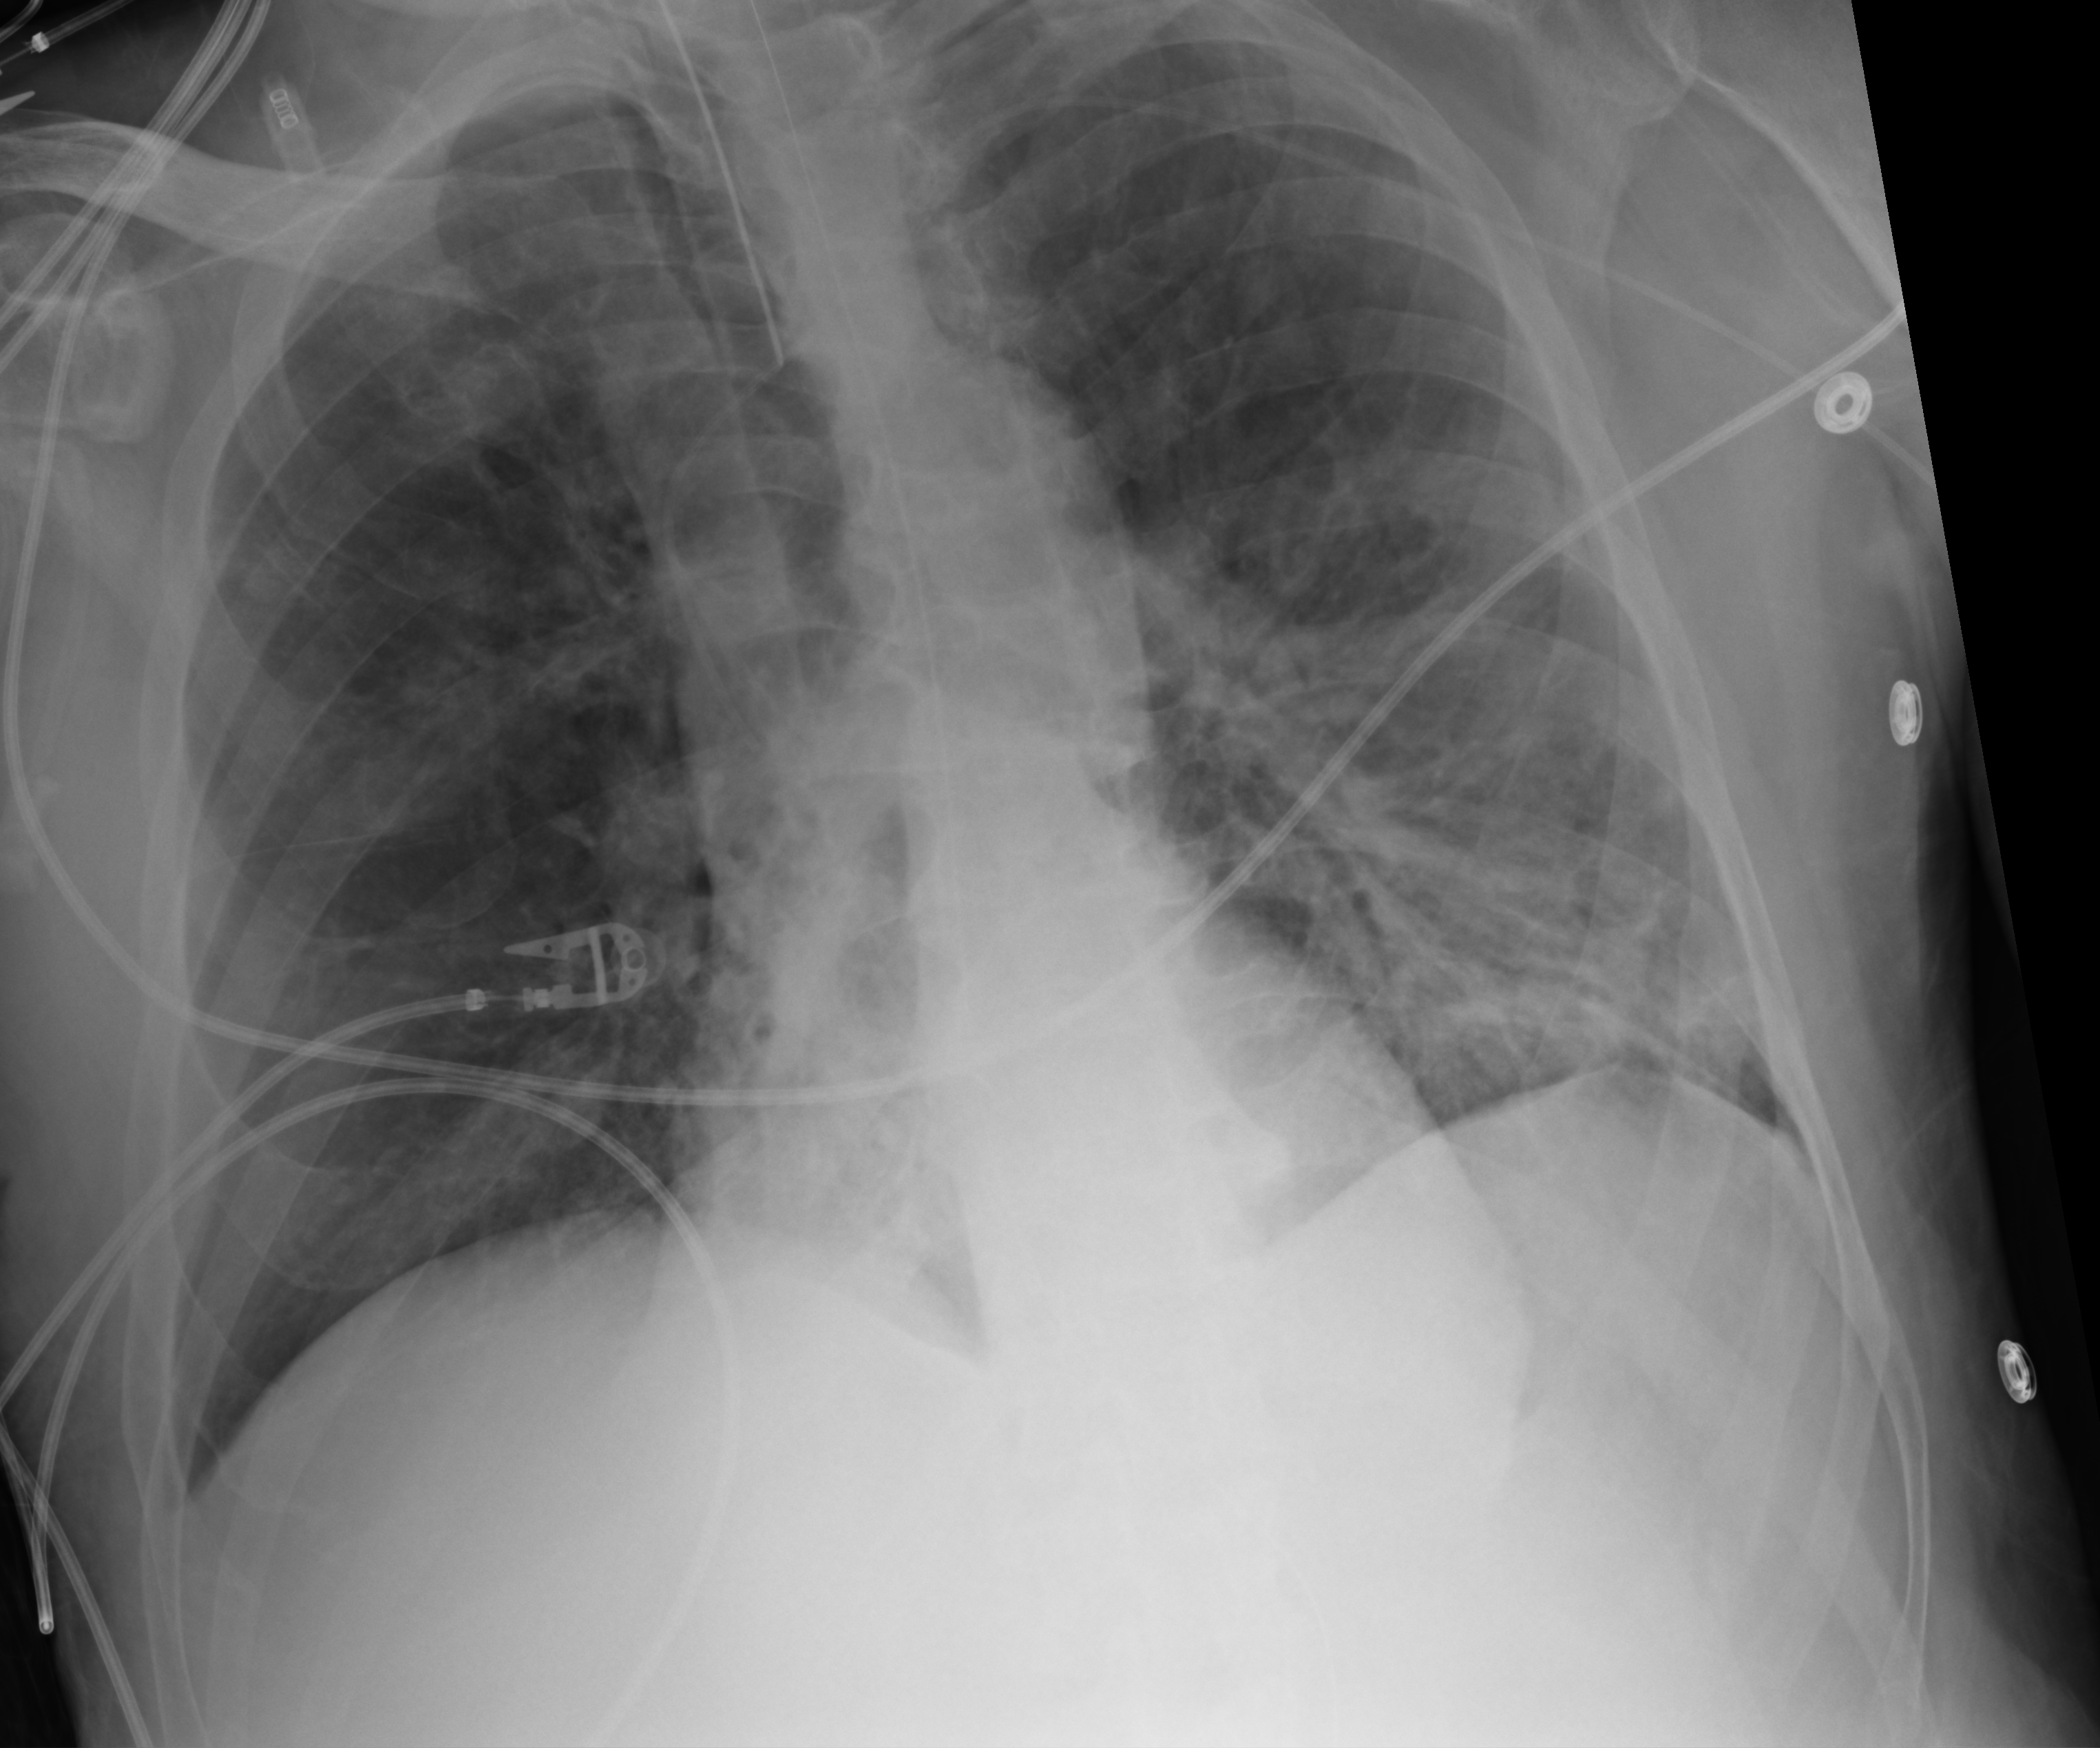
Chest X-ray (portable), anteroposterior (AP) projection. Patient hospitalised with COVID-19; male, aged 60–74 years.
Admission-level facts for this patient (not findings on this image; timing relative to this image not recorded): length of hospital stay: 35 days; mechanically ventilated during this hospital stay: yes.